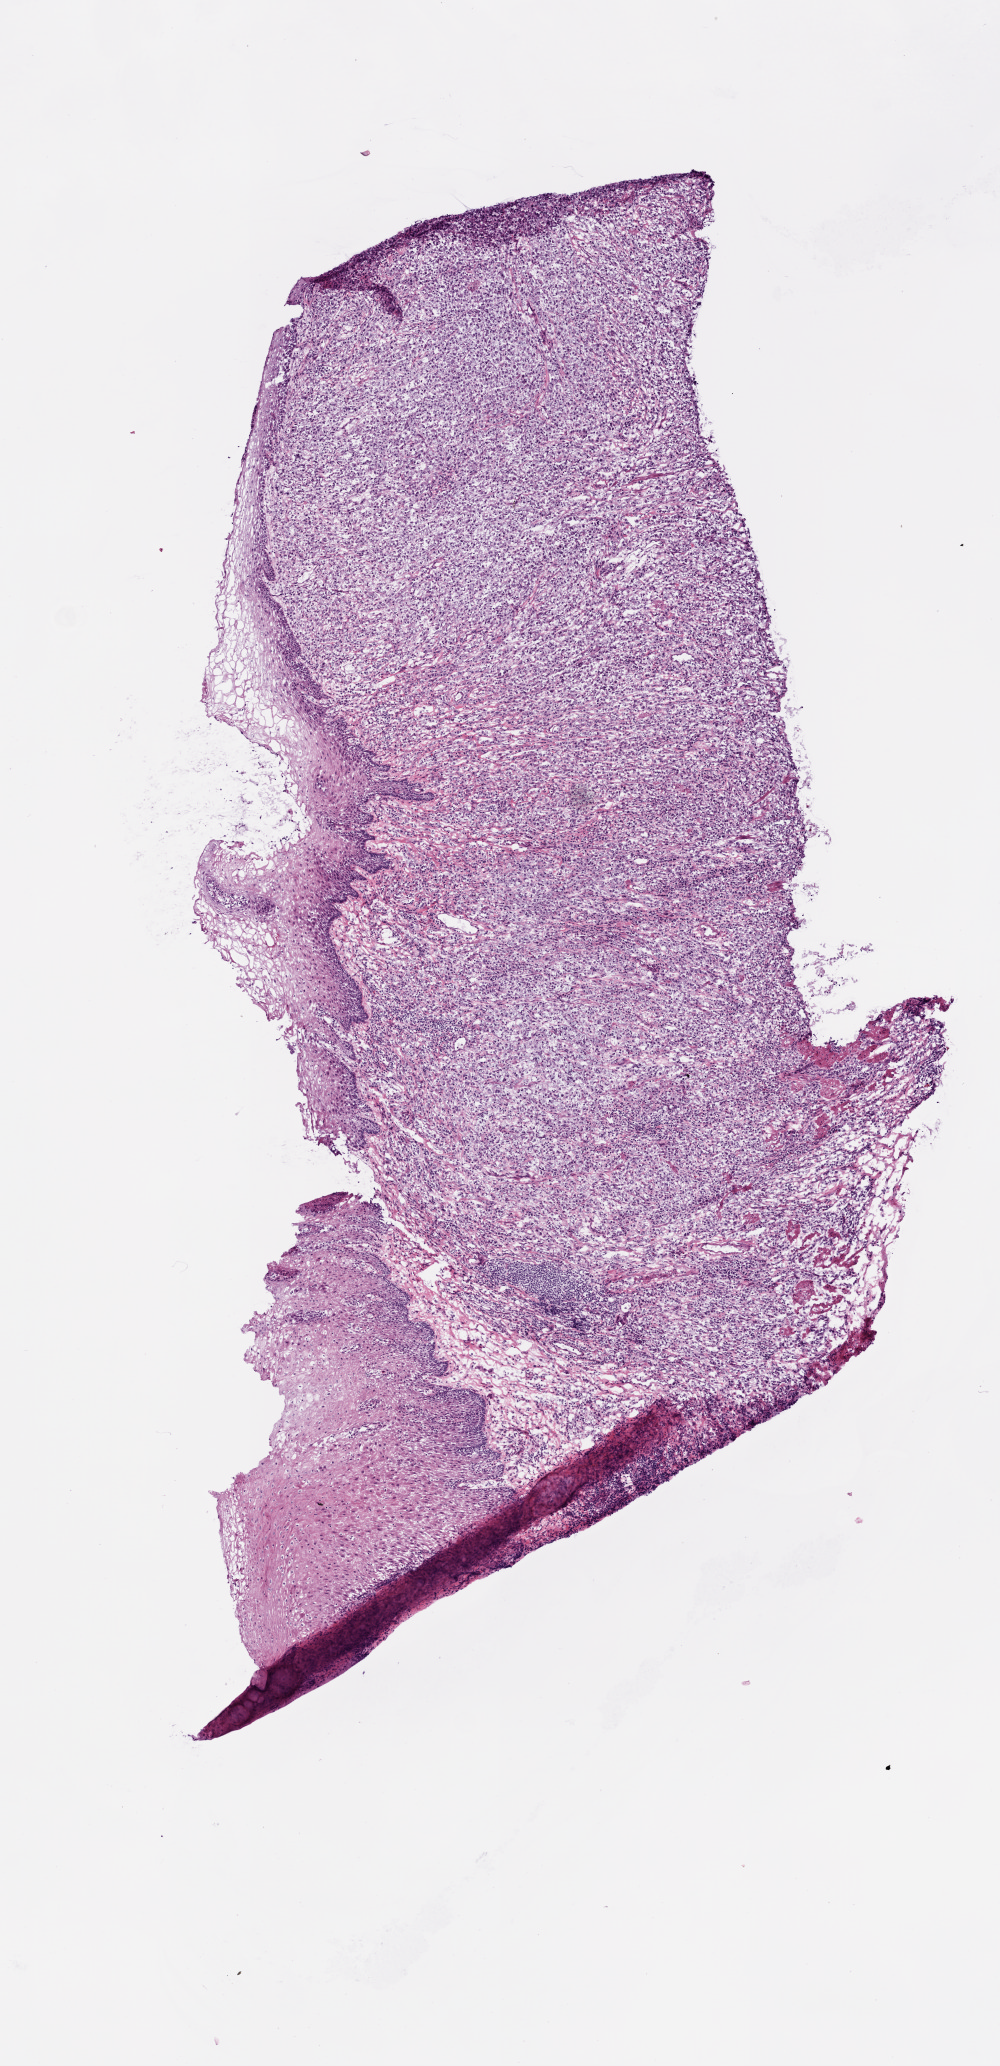
Digitized H&E tissue section (whole slide) — low-resolution overview of the scanned area, about 4.0 x 8.3 mm (acquisition: 20x scan), frozen section from the top of the tissue portion, stomach, primary tumour sample. Patient: male, age at initial diagnosis 58 years. Slide review estimates, as recorded: tumour cells 75%, tumour nuclei 80%.
Pathologic diagnosis: Adenocarcinoma, intestinal type (cardia, NOS).